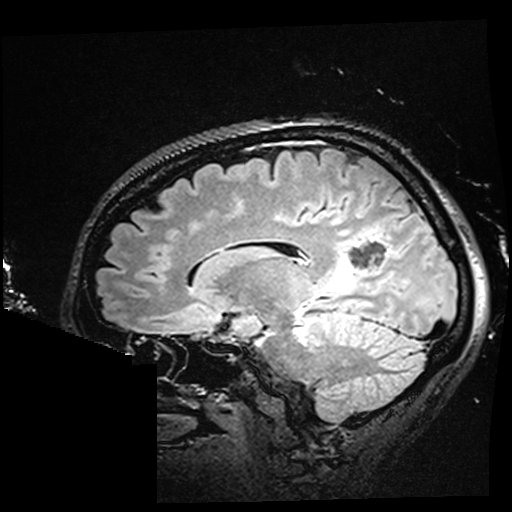
Brain MRI from a brain-tumour surgery series, one sagittal slice; slice 105 of 176 in the series (ordered by position); T2 FLAIR; 1 mm slice thickness; 512 × 512 image matrix, field of view 250 × 250 mm. From the clinical record (not read from this slice): histopathology: Oligodendroglioma; WHO grade: 2; IDH mutation: yes.
Outlined on this slice (outlined manually by an expert reader):
- residual tumour: bounding box [x1, y1, x2, y2] px = [323, 233, 367, 296]